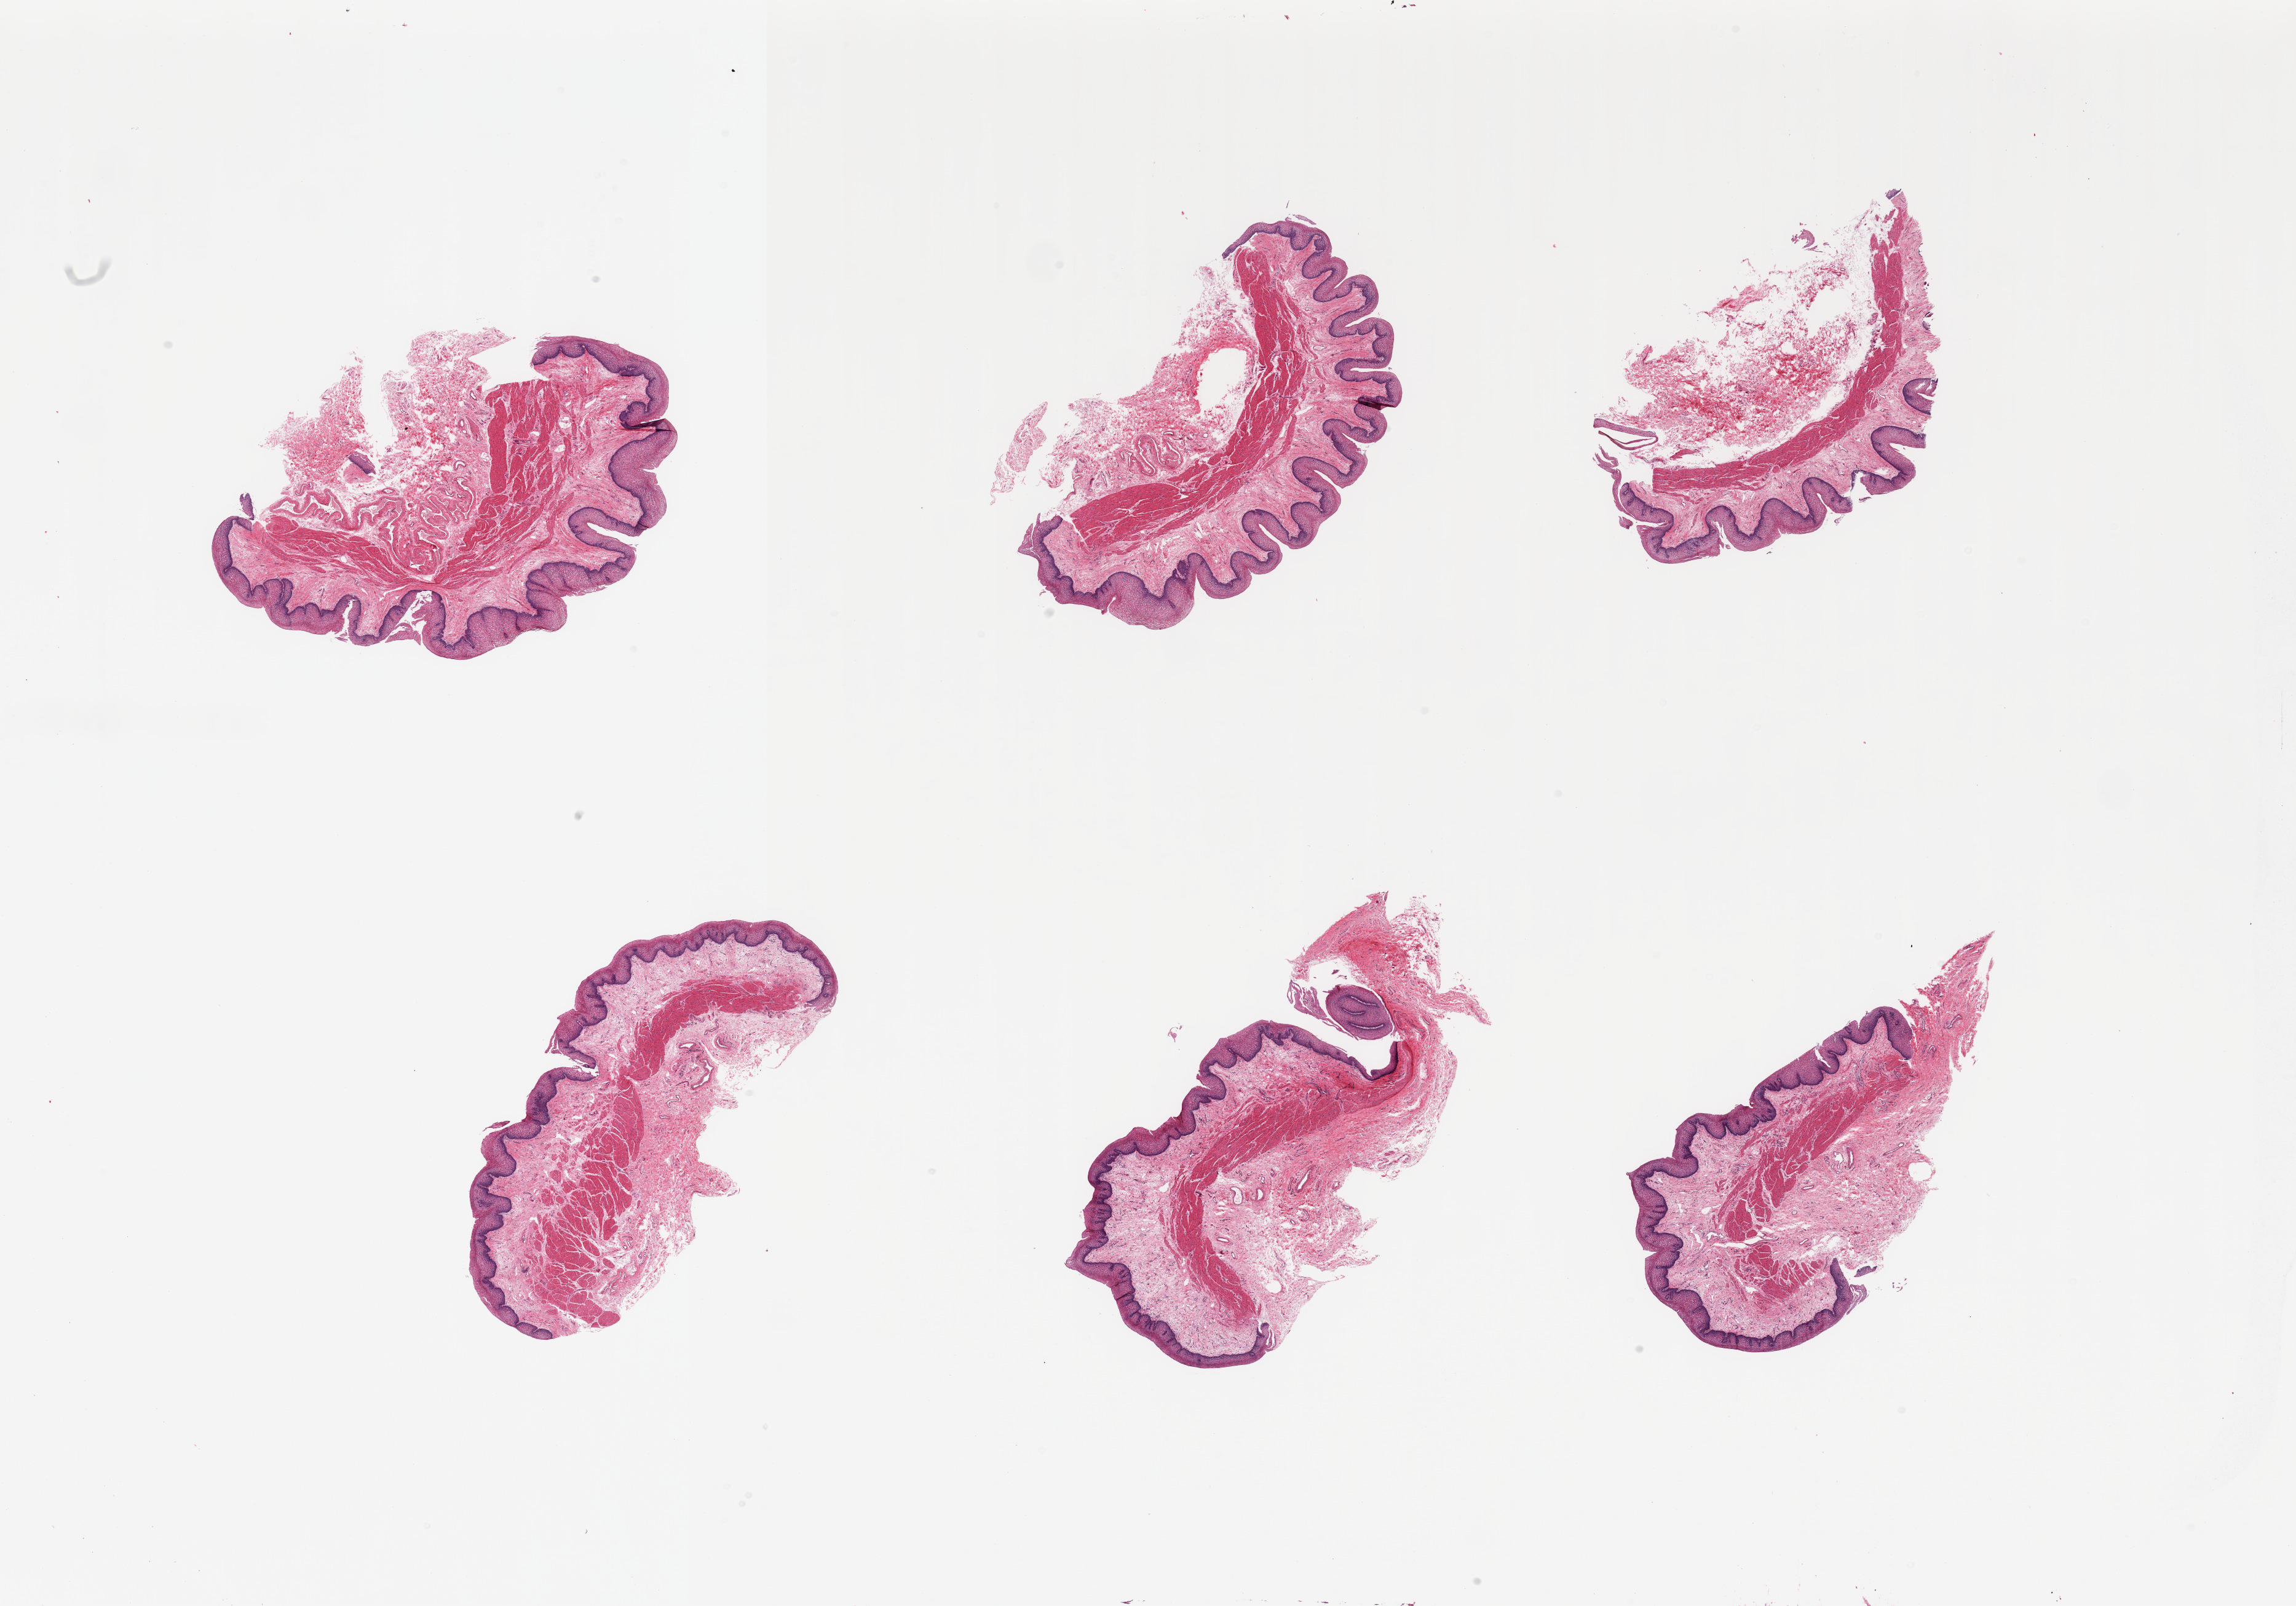
Whole-slide image, H&E stain — shown as a low-resolution overview of the whole scanned area (about 29.5 x 20.7 mm), PAXgene-fixed paraffin-embedded (PFPE) section, section of esophageal mucous membrane (target tissue), donor tissue sample. Donor: male.
Review note (as recorded): 6 pieces.